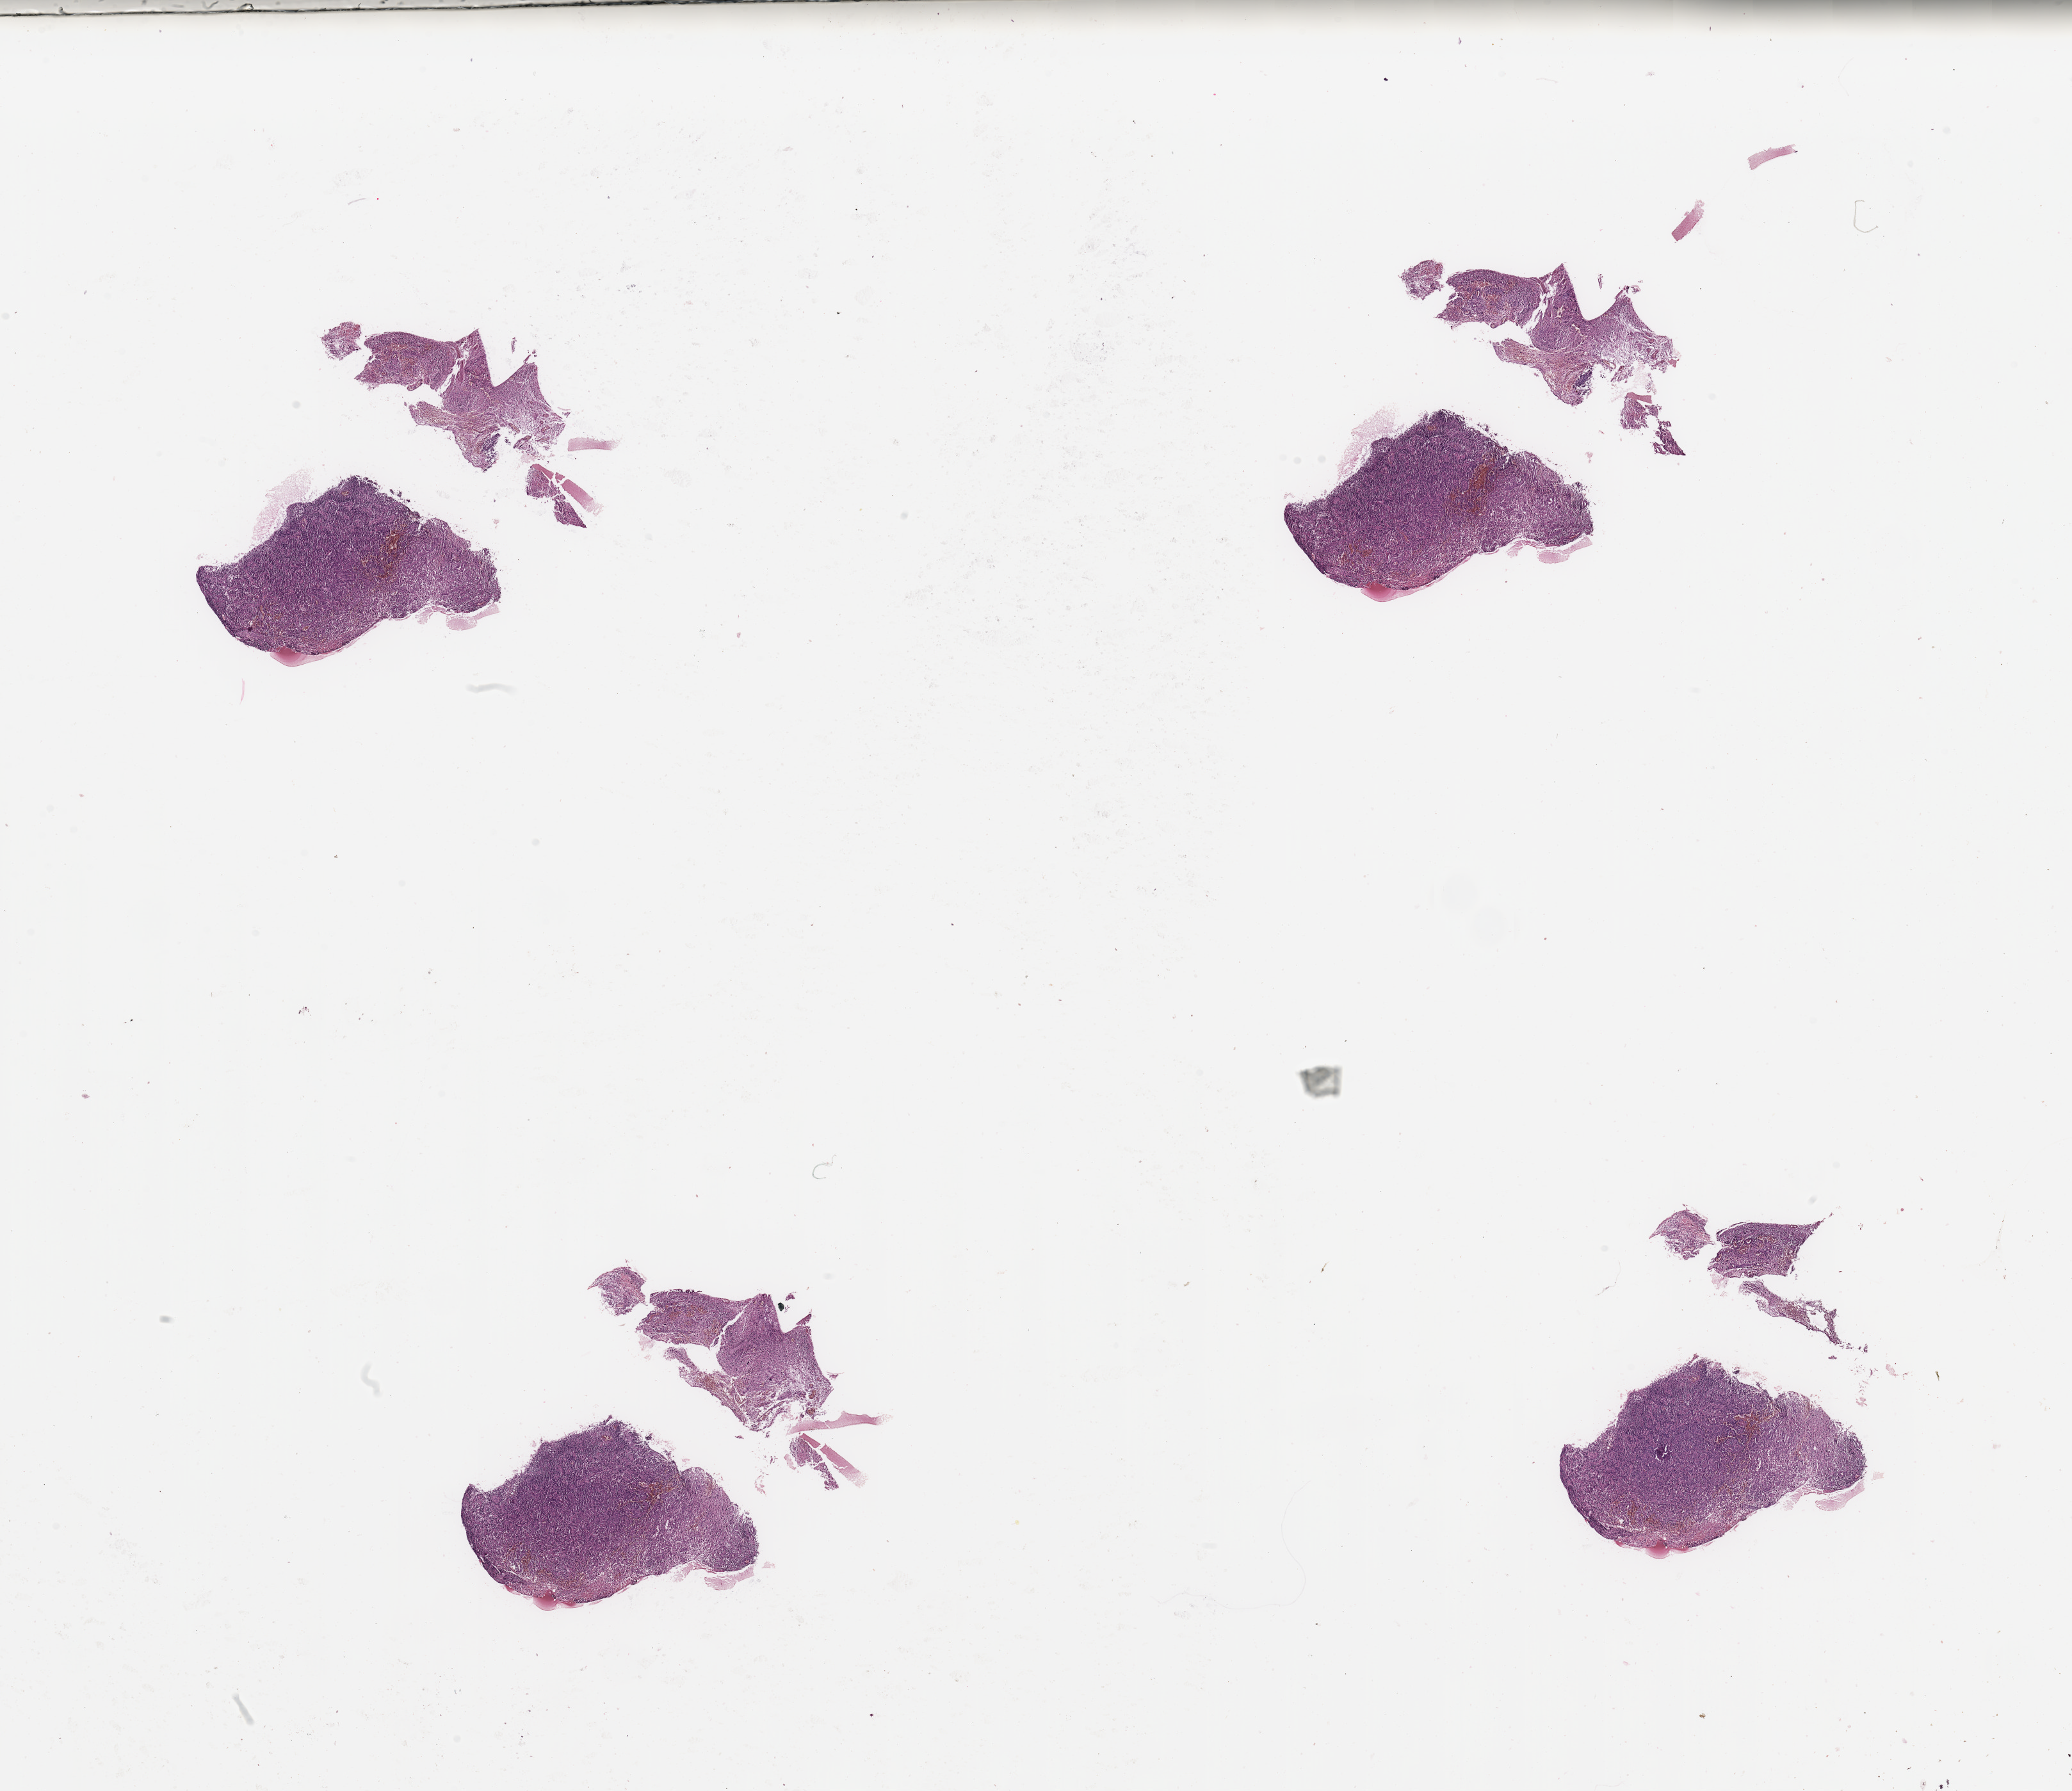
Digitized Hematoxylin and eosin (H&E) stained tissue section (whole slide) — a low-resolution overview of the entire scanned area, about 25.6 x 22.1 mm; tumour tissue sample, sampled site: brain. Patient: female, age 58 years.
Diagnosis: Glioblastoma.